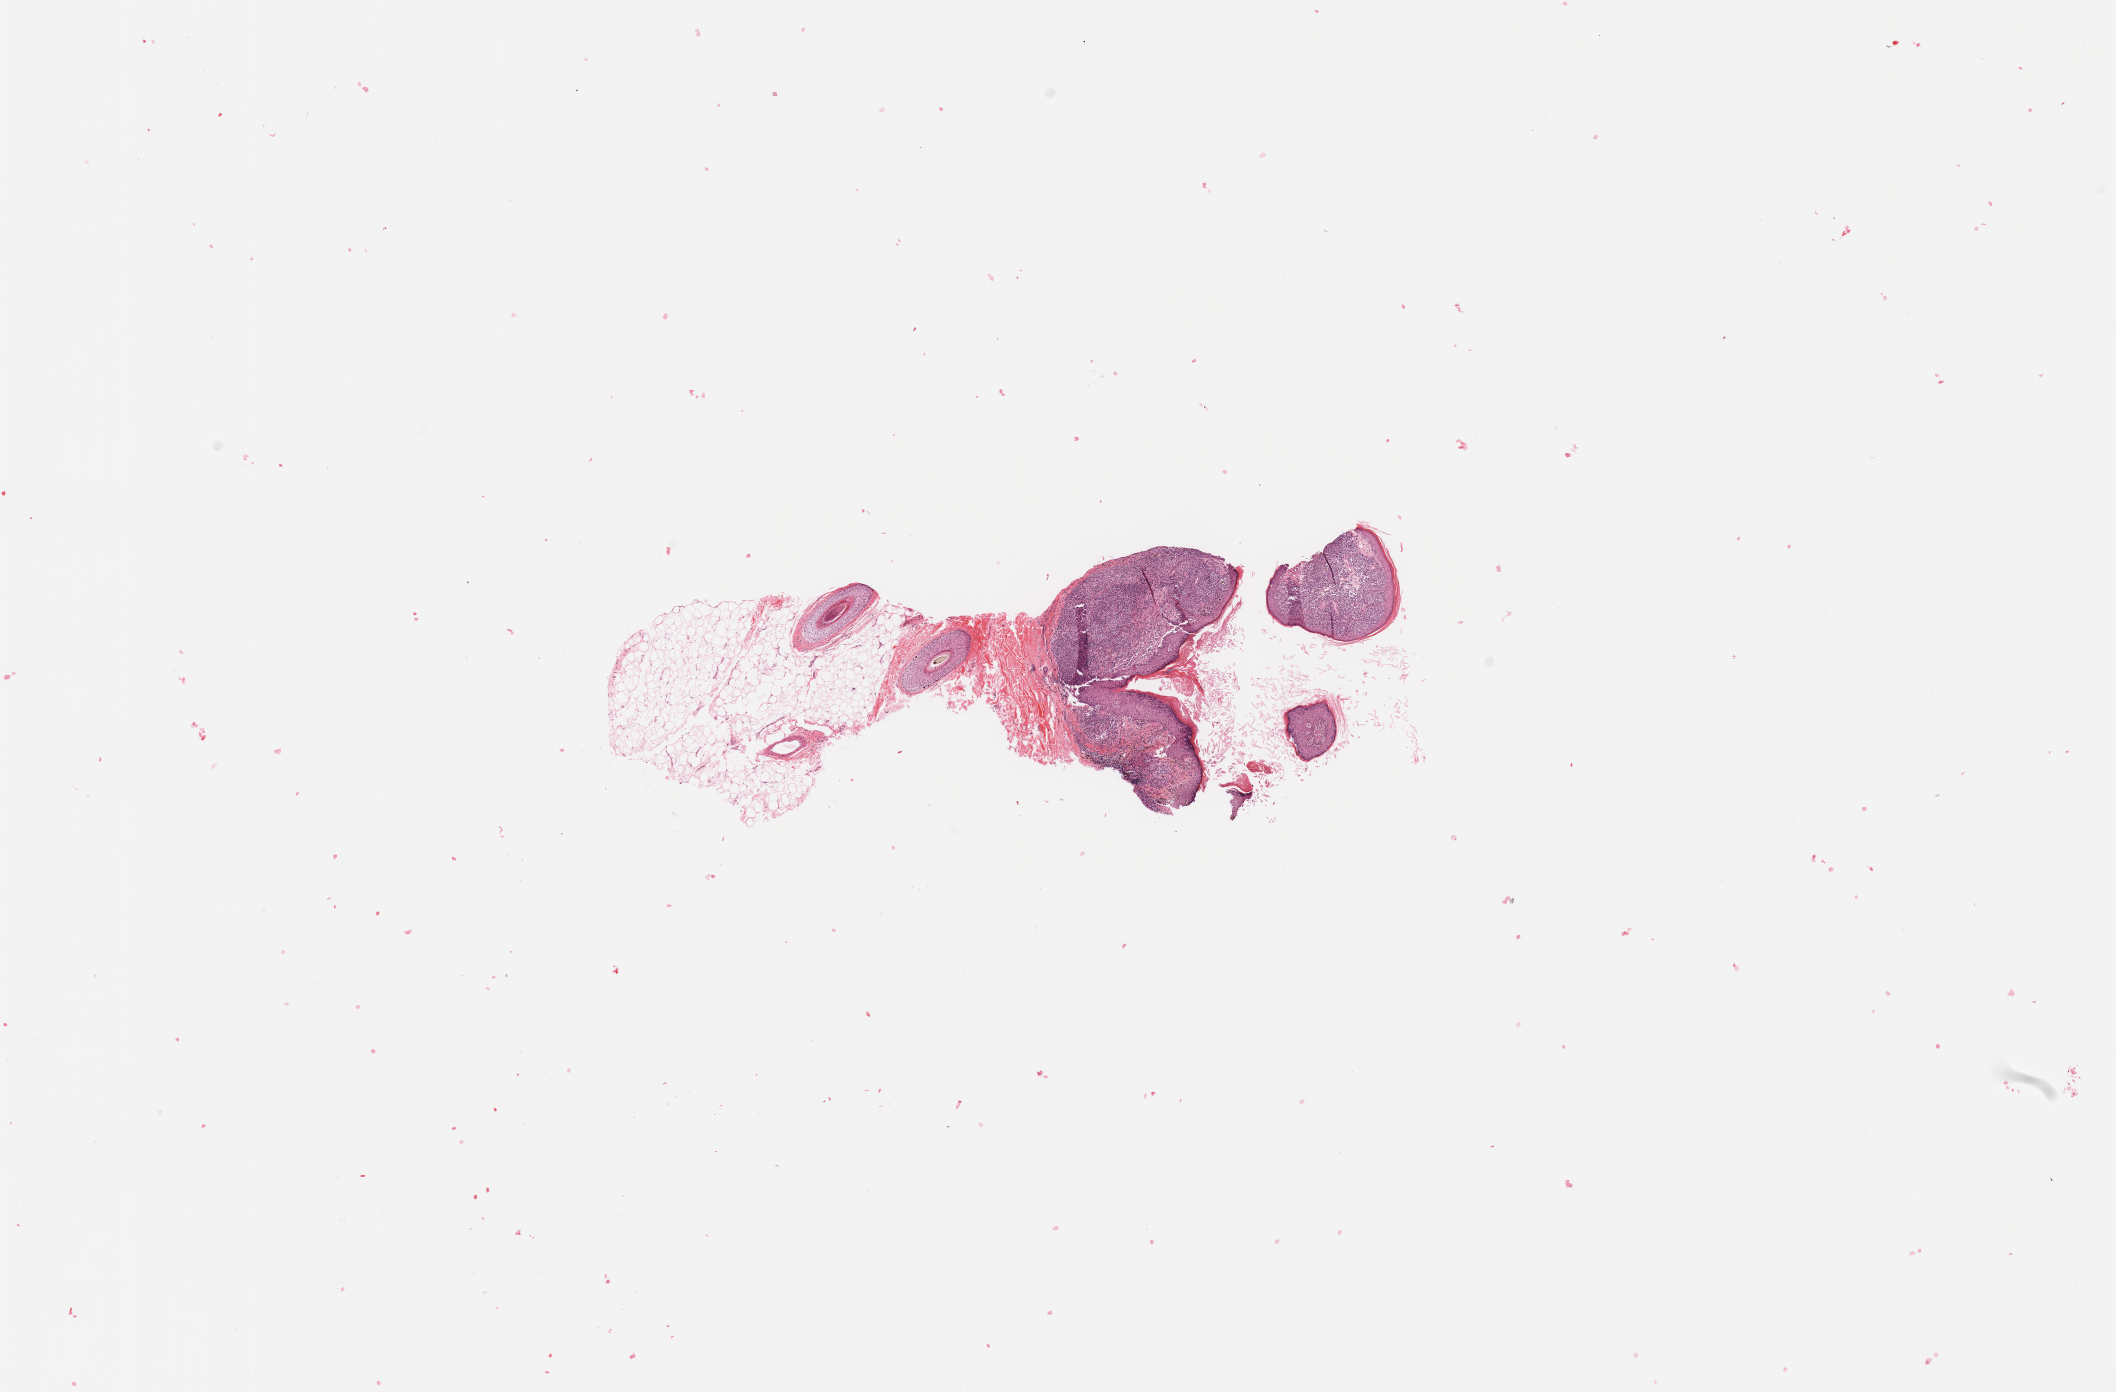
Whole-slide histology image, H&E-stained, a low-resolution overview of the entire scanned area, about 16.7 x 11.0 mm (acquisition: 20x scan). Melanoma tumour tissue; sampled site not recorded. Female, 73 y/o.
- primary tumour site (as recorded): head & neck
- histologic diagnosis: Malignant melanoma, NOS
- AJCC pathologic stage: IIA